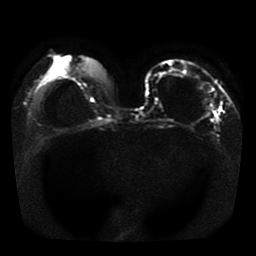
Breast MRI, one axial slice; diffusion-weighted series; image 2 of 4 stored at this slice position (different b-values; order by instance number); 1.5 T; 5 mm slice thickness; 256 × 256 image matrix, field of view 330 × 330 mm. Female patient.
Outlined on this slice (expert manual segmentation):
- tumour on diffusion-weighted imaging: bounding box <202,106,214,119> (left, top, right, bottom; pixels)